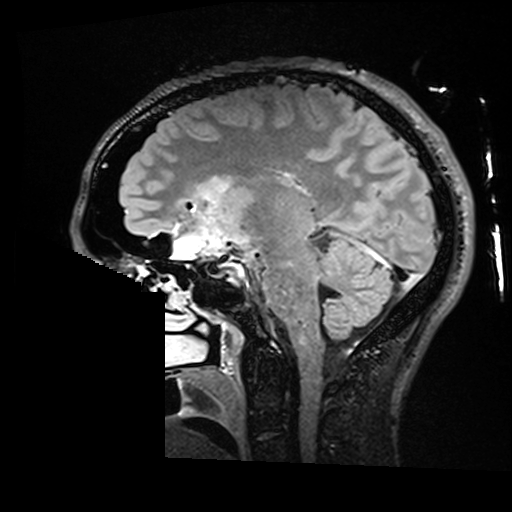
Brain MRI from a brain-tumour surgery series, one sagittal slice; position 95 of 176 along the scan axis; T2 FLAIR; 512 × 512 image matrix, field of view 250 × 250 mm. From the clinical record (not read from this slice): histopathology: Astrocytoma; WHO grade: 2; IDH mutation: yes; tumour location: Right Insular.
Structures marked on this image (expert manual segmentation):
- residual tumour: bounding box <199,177,230,204> (left, top, right, bottom; pixels)